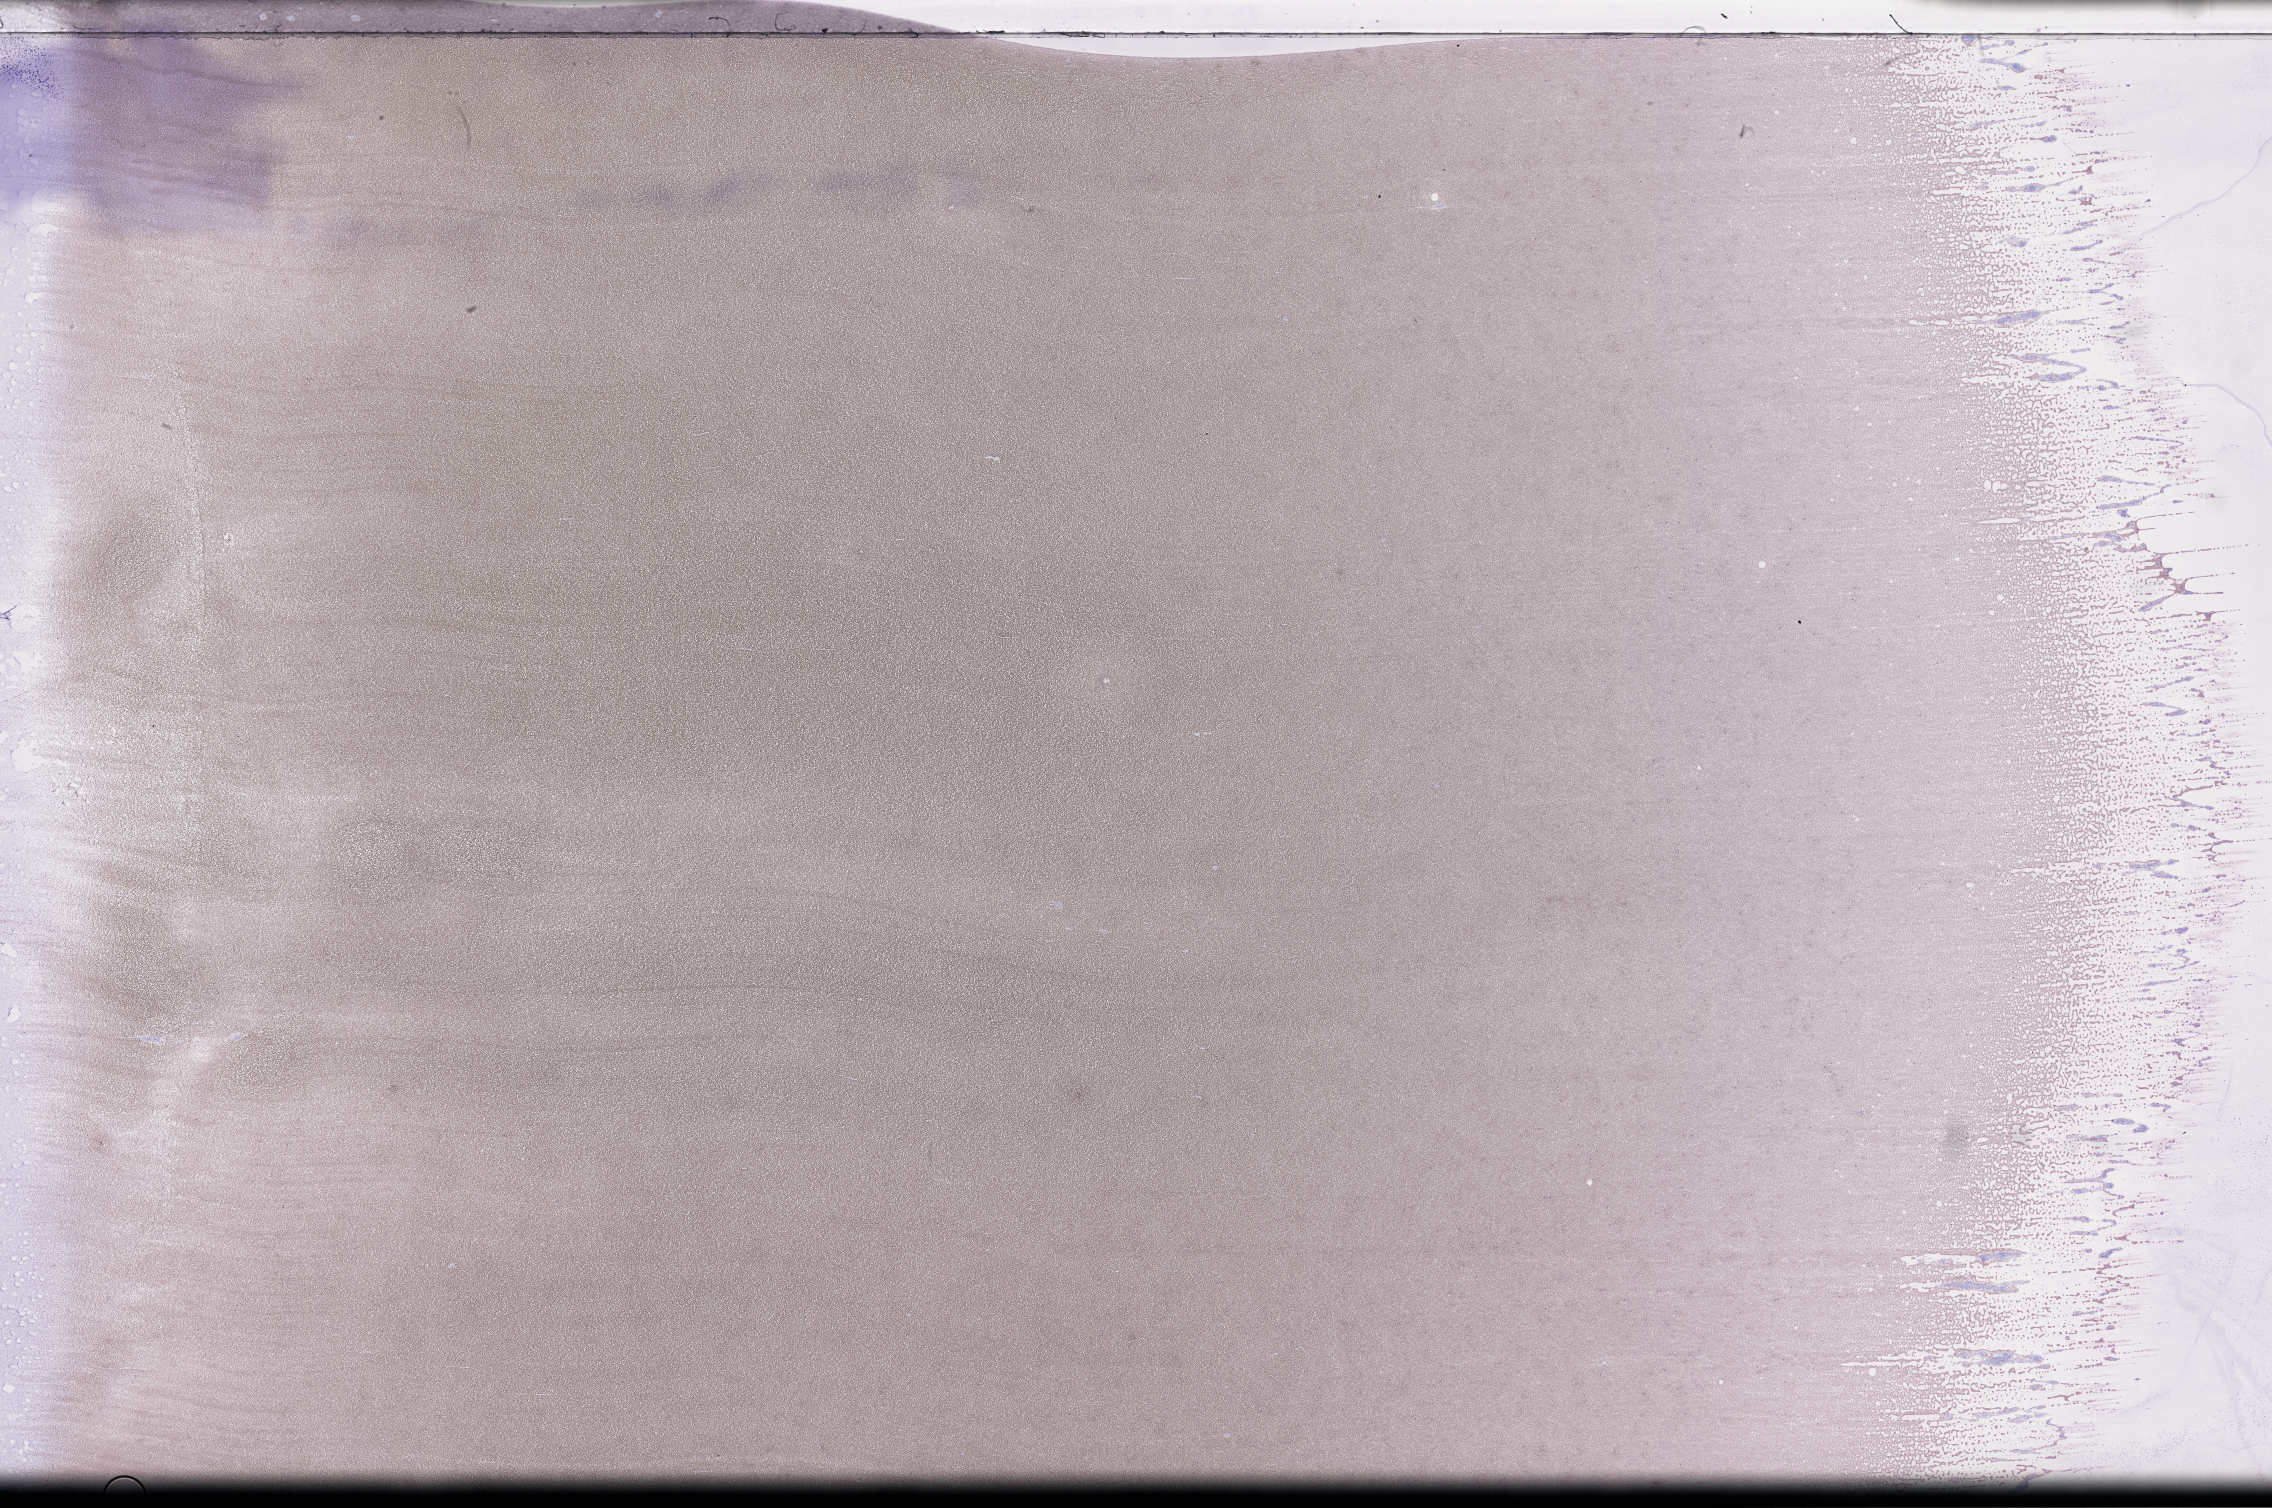
Whole-slide image of a whole blood smear, Wright–Giemsa stain — low-resolution overview of the scanned area, about 36.7 x 24.4 mm, specimen time point: collected on treatment. Patient: male.
- patient diagnosis: Plasma Cell Myeloma